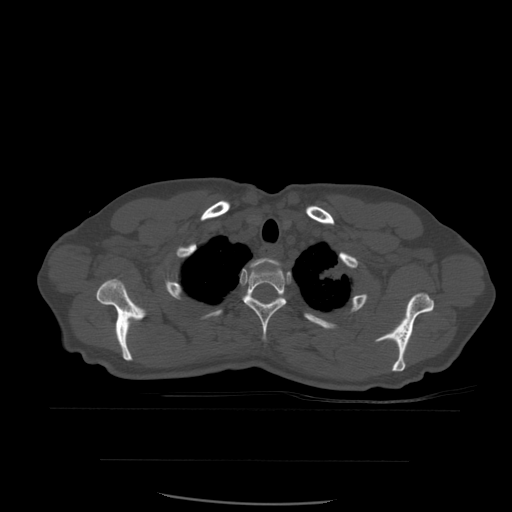
CT including the spine, one axial slice. Slice 456 of 574 in the series (ordered by position). Bone window (W 1800 / L 400 HU). 1.25 mm slice thickness. 512 × 512 image matrix, field of view 392 × 392 mm. Patient age 48 years. From the clinical record (not read from this slice): primary cancer: lung; vertebrae with lytic lesions (as recorded): T11.
Outlined on this slice (semi-automatic segmentation, software-assisted and operator-edited):
- T1 vertebra: bounding box [x1, y1, x2, y2] px = [251, 258, 279, 268]
- T2 vertebra: [242, 259, 287, 342]
- T3 vertebra: [229, 299, 273, 317]